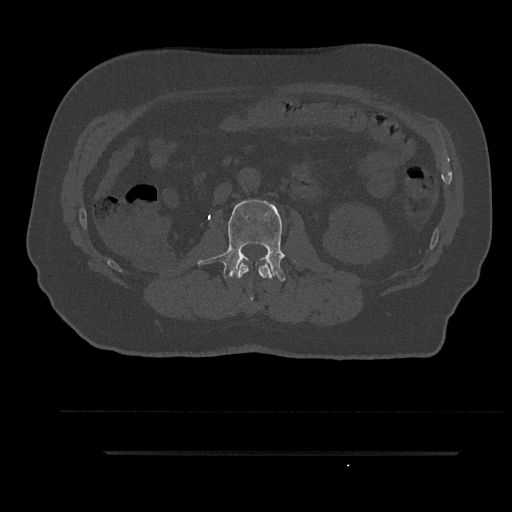
CT including the spine, one axial slice; reconstruction kernel Br40s/3; bone window (W 1800 / L 400 HU); 512 × 512 image matrix, field of view 432 × 432 mm. Patient: male, 63 years. Case-level facts recorded for this patient, not image findings: primary cancer: renal.
Structures marked on this image (semi-automatic segmentation, software-assisted and operator-edited):
- L1 vertebra: bounding box (x1, y1, x2, y2) in pixels: (237, 260, 275, 301)
- L2 vertebra: (198, 199, 285, 282)